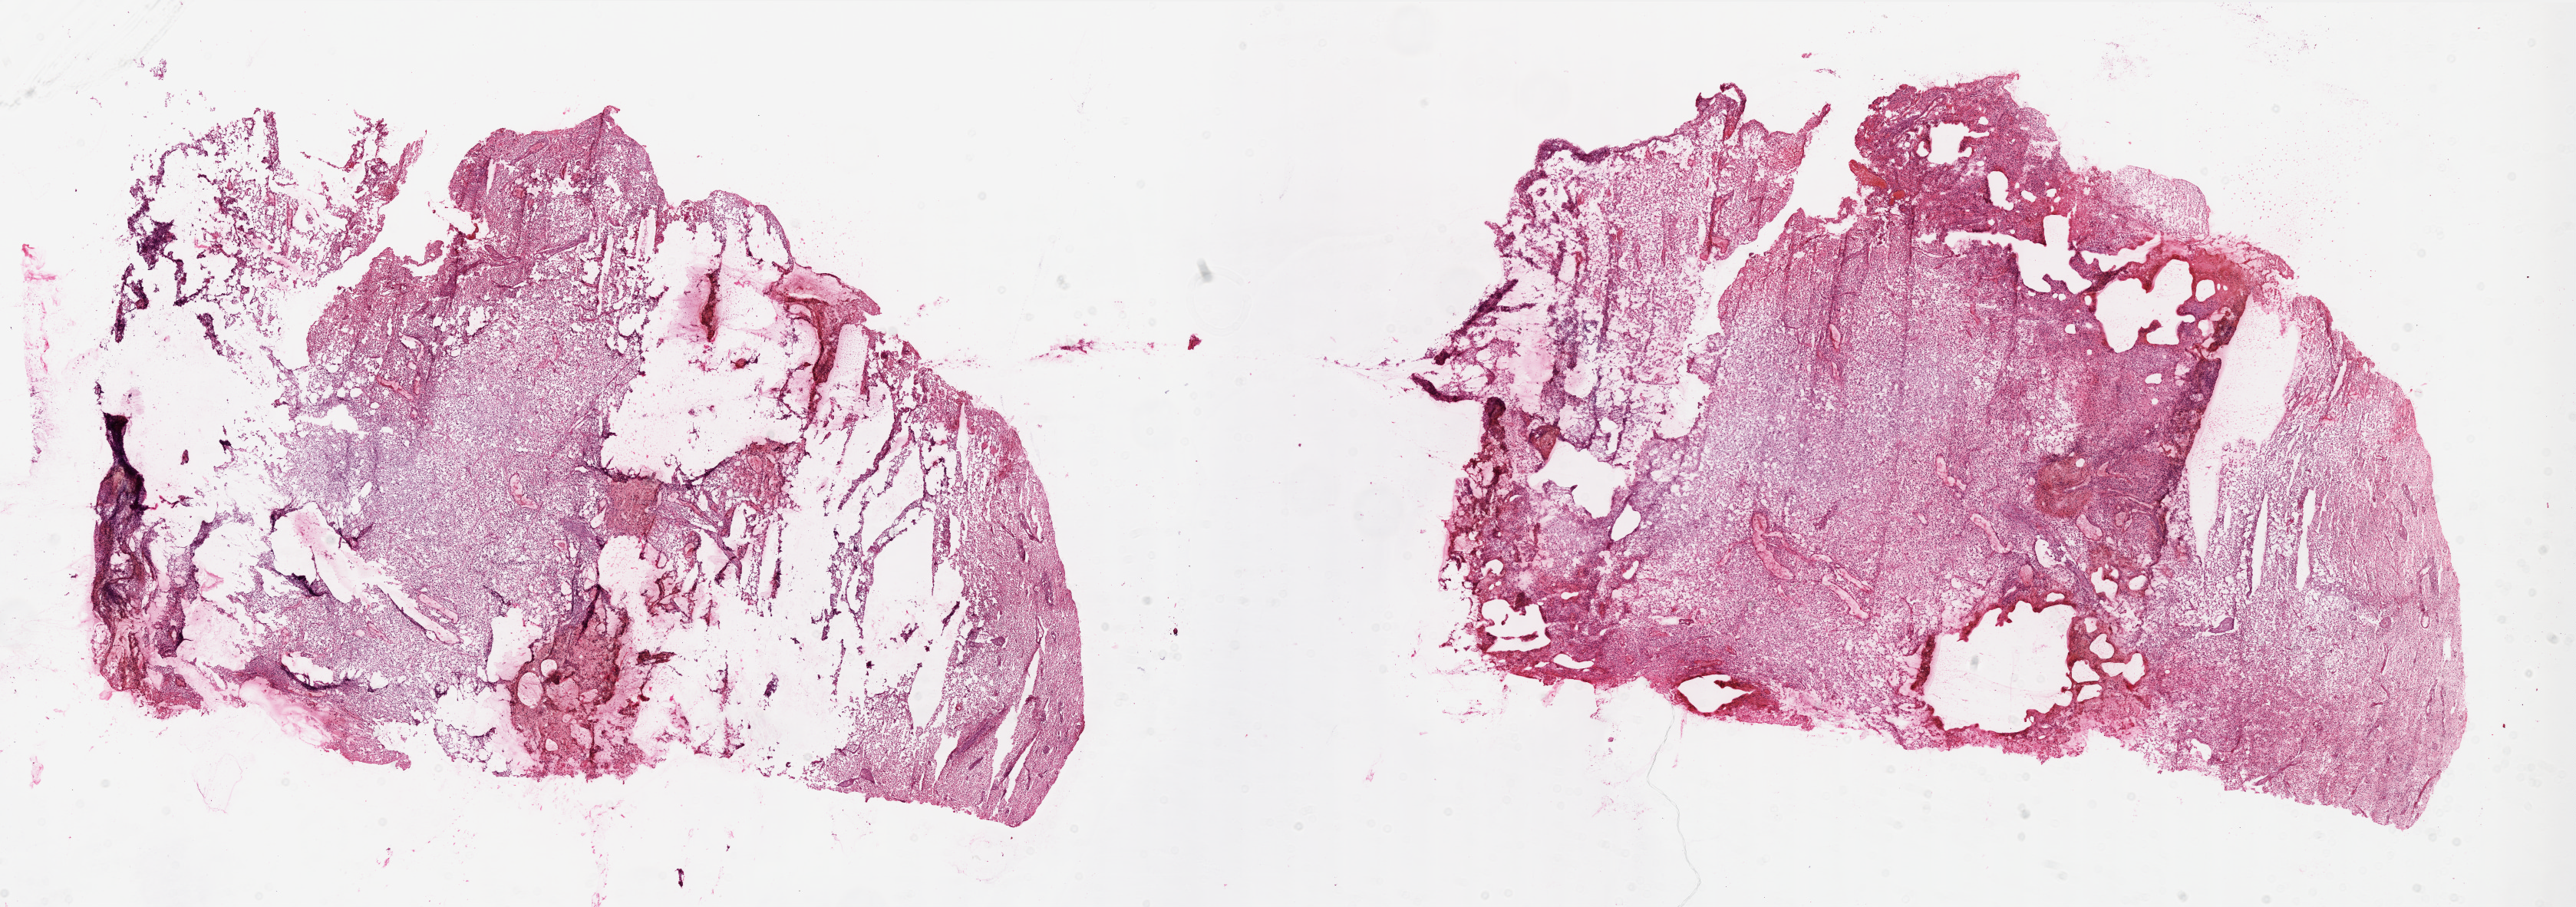
Whole-slide histology image, H&E-stained, whole scanned area (about 27.0 x 9.5 mm) shown as a low-resolution overview, frozen section, primary tumour sample from the brain. Male patient; age at initial diagnosis 50 years. Pathologist review of this section (percent, as recorded): tumour cells 95%, tumour nuclei 100%, normal cells 0%, stromal cells 0%, necrosis 5%.
Histologic diagnosis: Glioblastoma.